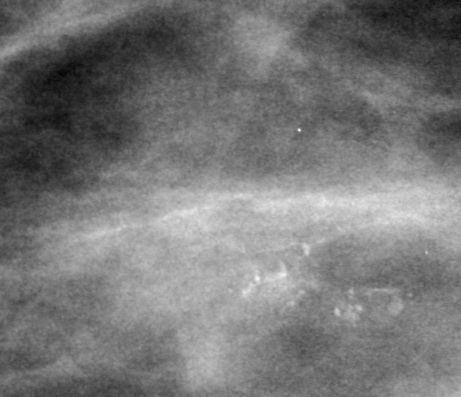
Cropped region of a digitized screen-film mammogram centred on a radiologist-marked abnormality, left breast, CC view.
- Calcifications, morphology amorphous, distribution clustered; BI-RADS assessment category 0 (incomplete: needs additional imaging); pathology result (as recorded, not read from the image): benign.